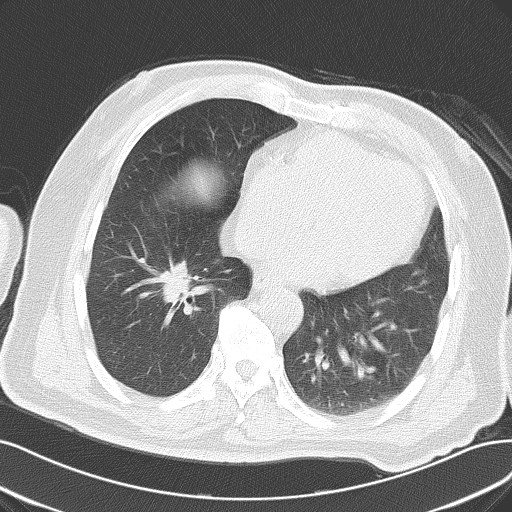
Chest CT, one axial slice. Position 27 of 61 along the scan axis. Reconstruction kernel B70f. Lung window (W 1500 / L -600 HU). 512 × 512 image matrix, field of view 363 × 363 mm. Patient: male, 69 years. Case-level facts recorded for this patient, not image findings: clinical TNM (as recorded): T1c N0 M0; histopathological grade: G2-3.
Structures marked on this image (rectangle marked by the reading radiologist):
- lung tumour (recorded histology: adenocarcinoma): bounding box (x1, y1, x2, y2) in pixels: (144, 252, 198, 306)